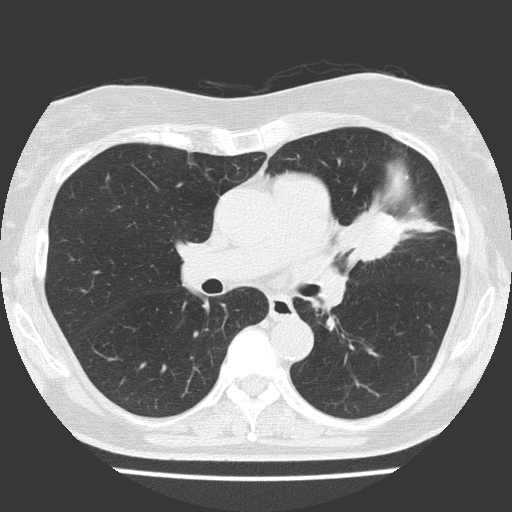
Low-dose screening chest CT, one axial slice. Position 84 of 151 along the scan axis. Lung window (W 1500 / L -600 HU). 2 mm slice thickness. 512 × 512 image matrix, field of view 309 × 309 mm.
Structures marked on this image (expert manual segmentation):
- lesion 1 (tumor, upper lobe of left lung): bounding box [x1, y1, x2, y2] px = [343, 209, 402, 261]